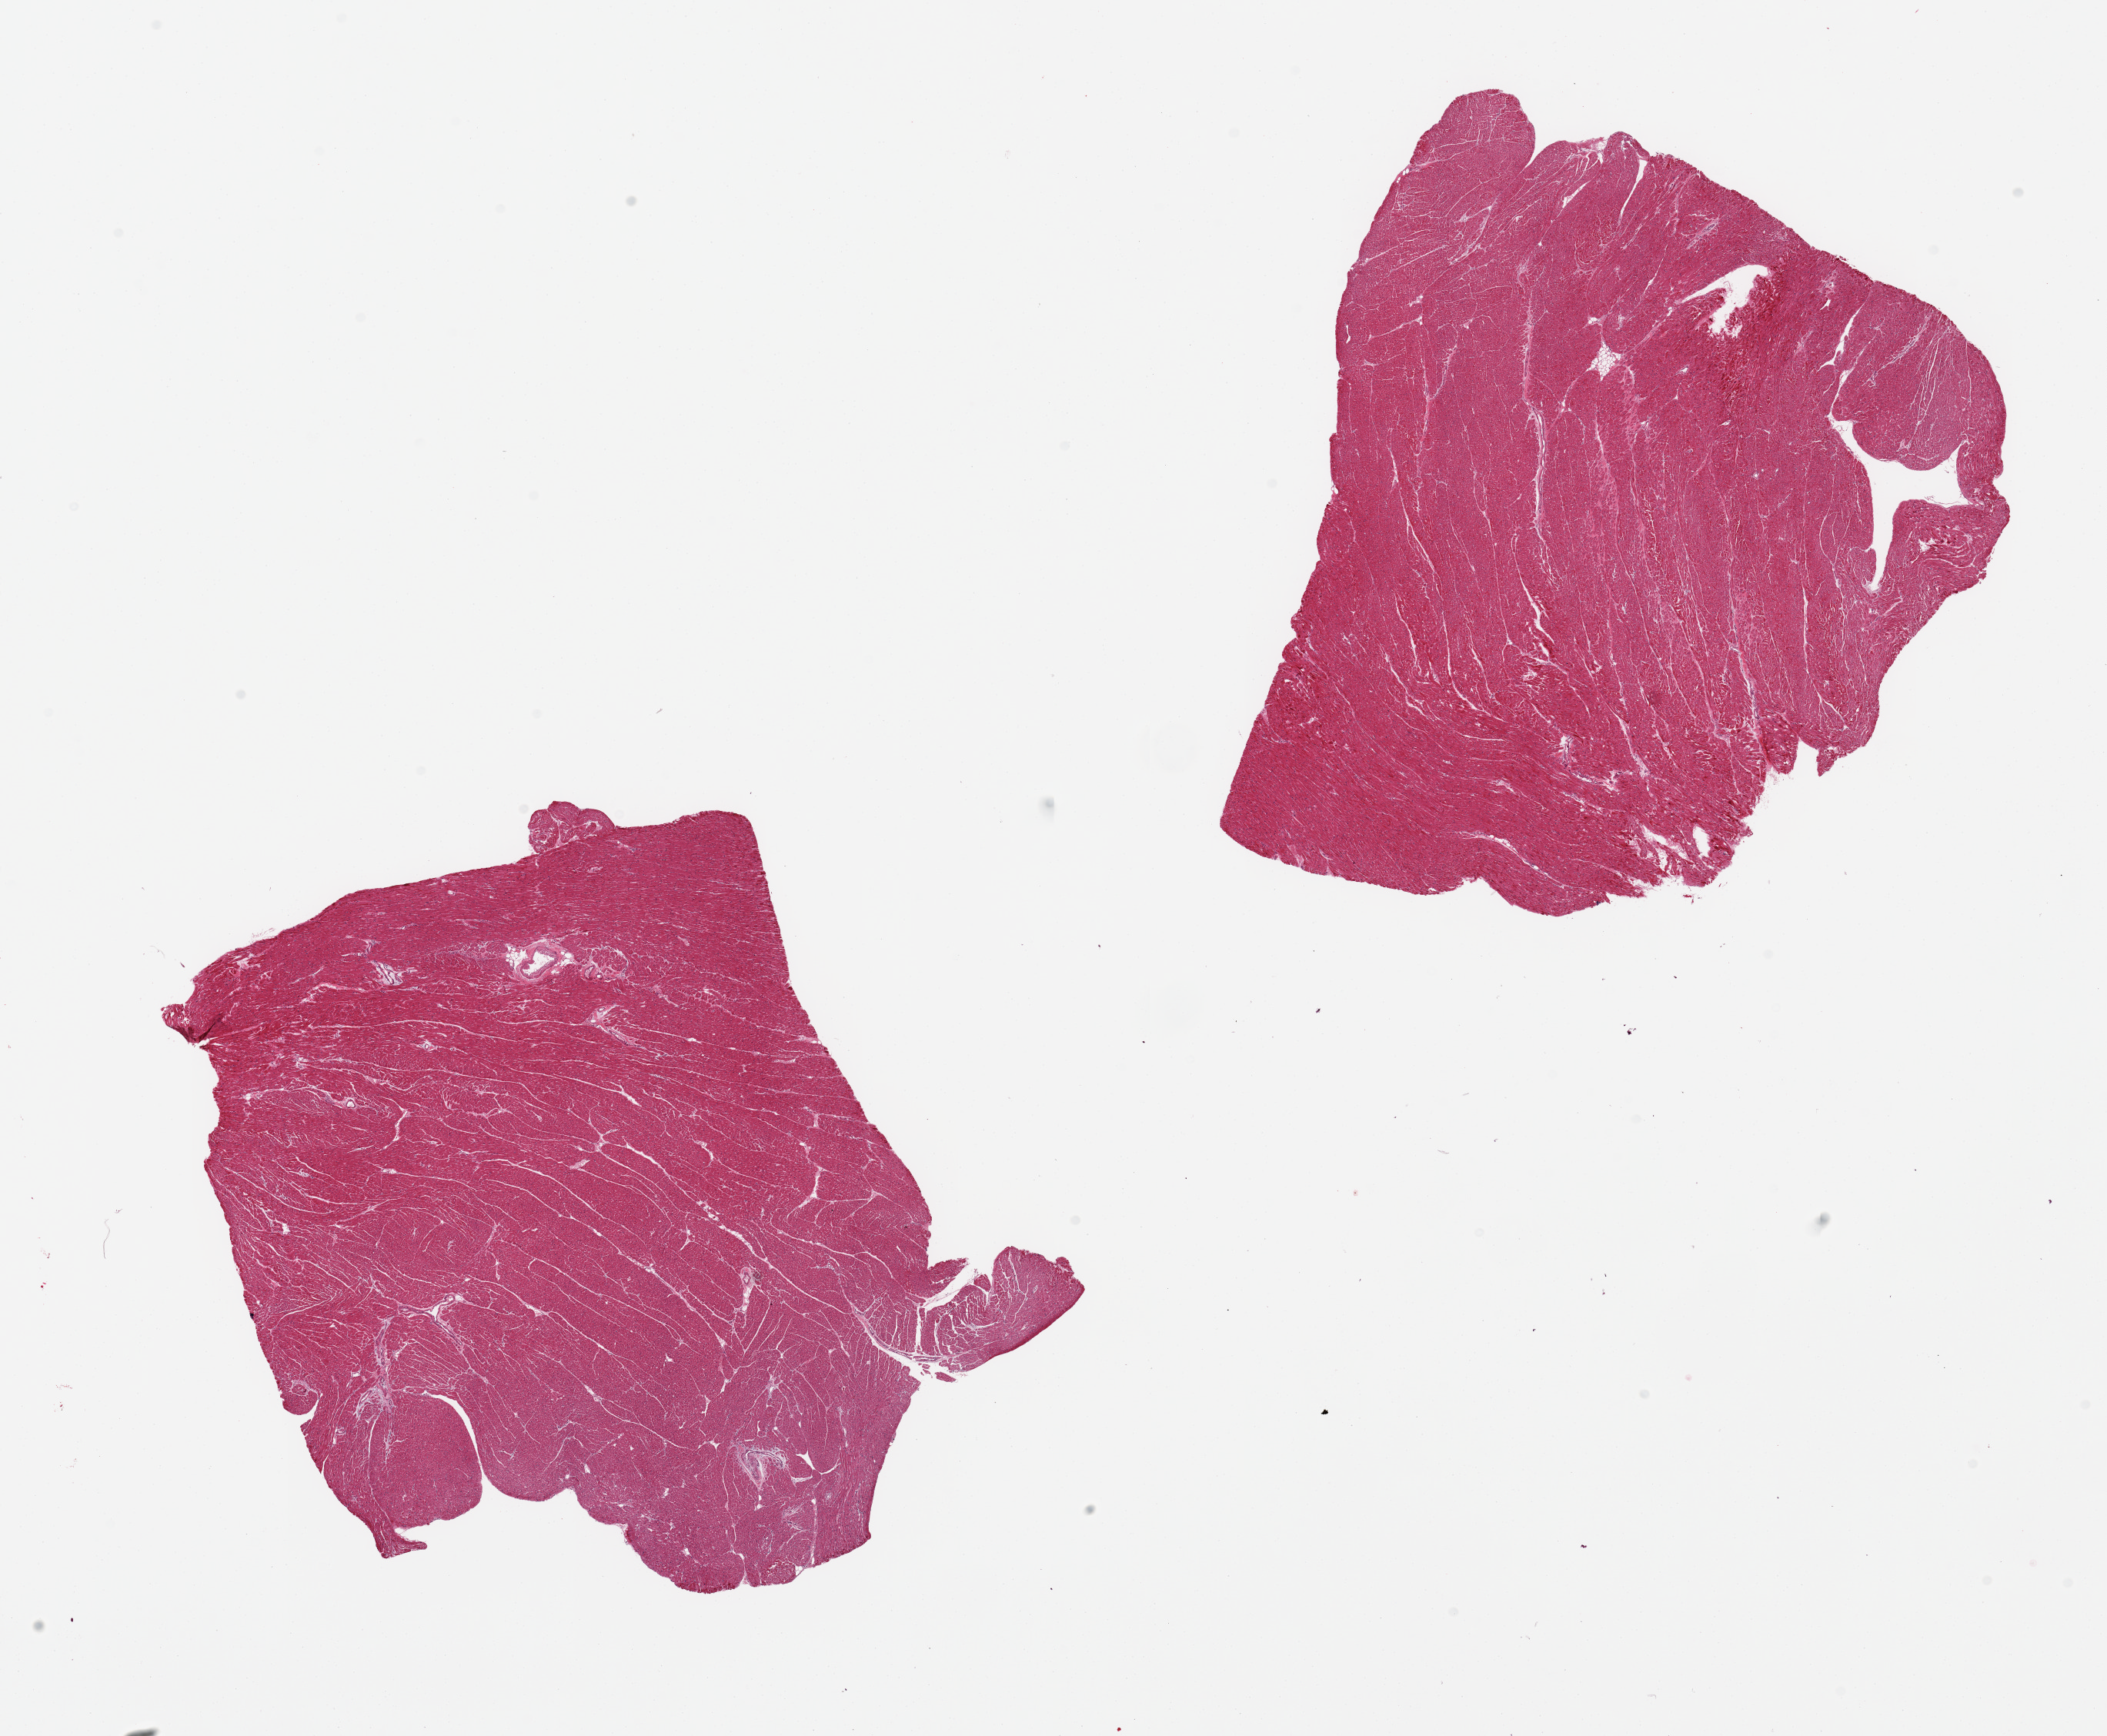
Hematoxylin and eosin (H&E) whole-slide image, shown as a low-resolution overview of the whole scanned area (about 21.7 x 17.8 mm); PAXgene-fixed paraffin-embedded (PFPE) section; sampled site (target tissue): heart; donor tissue sample.
* review note (as recorded): 2 pieces; no lesions